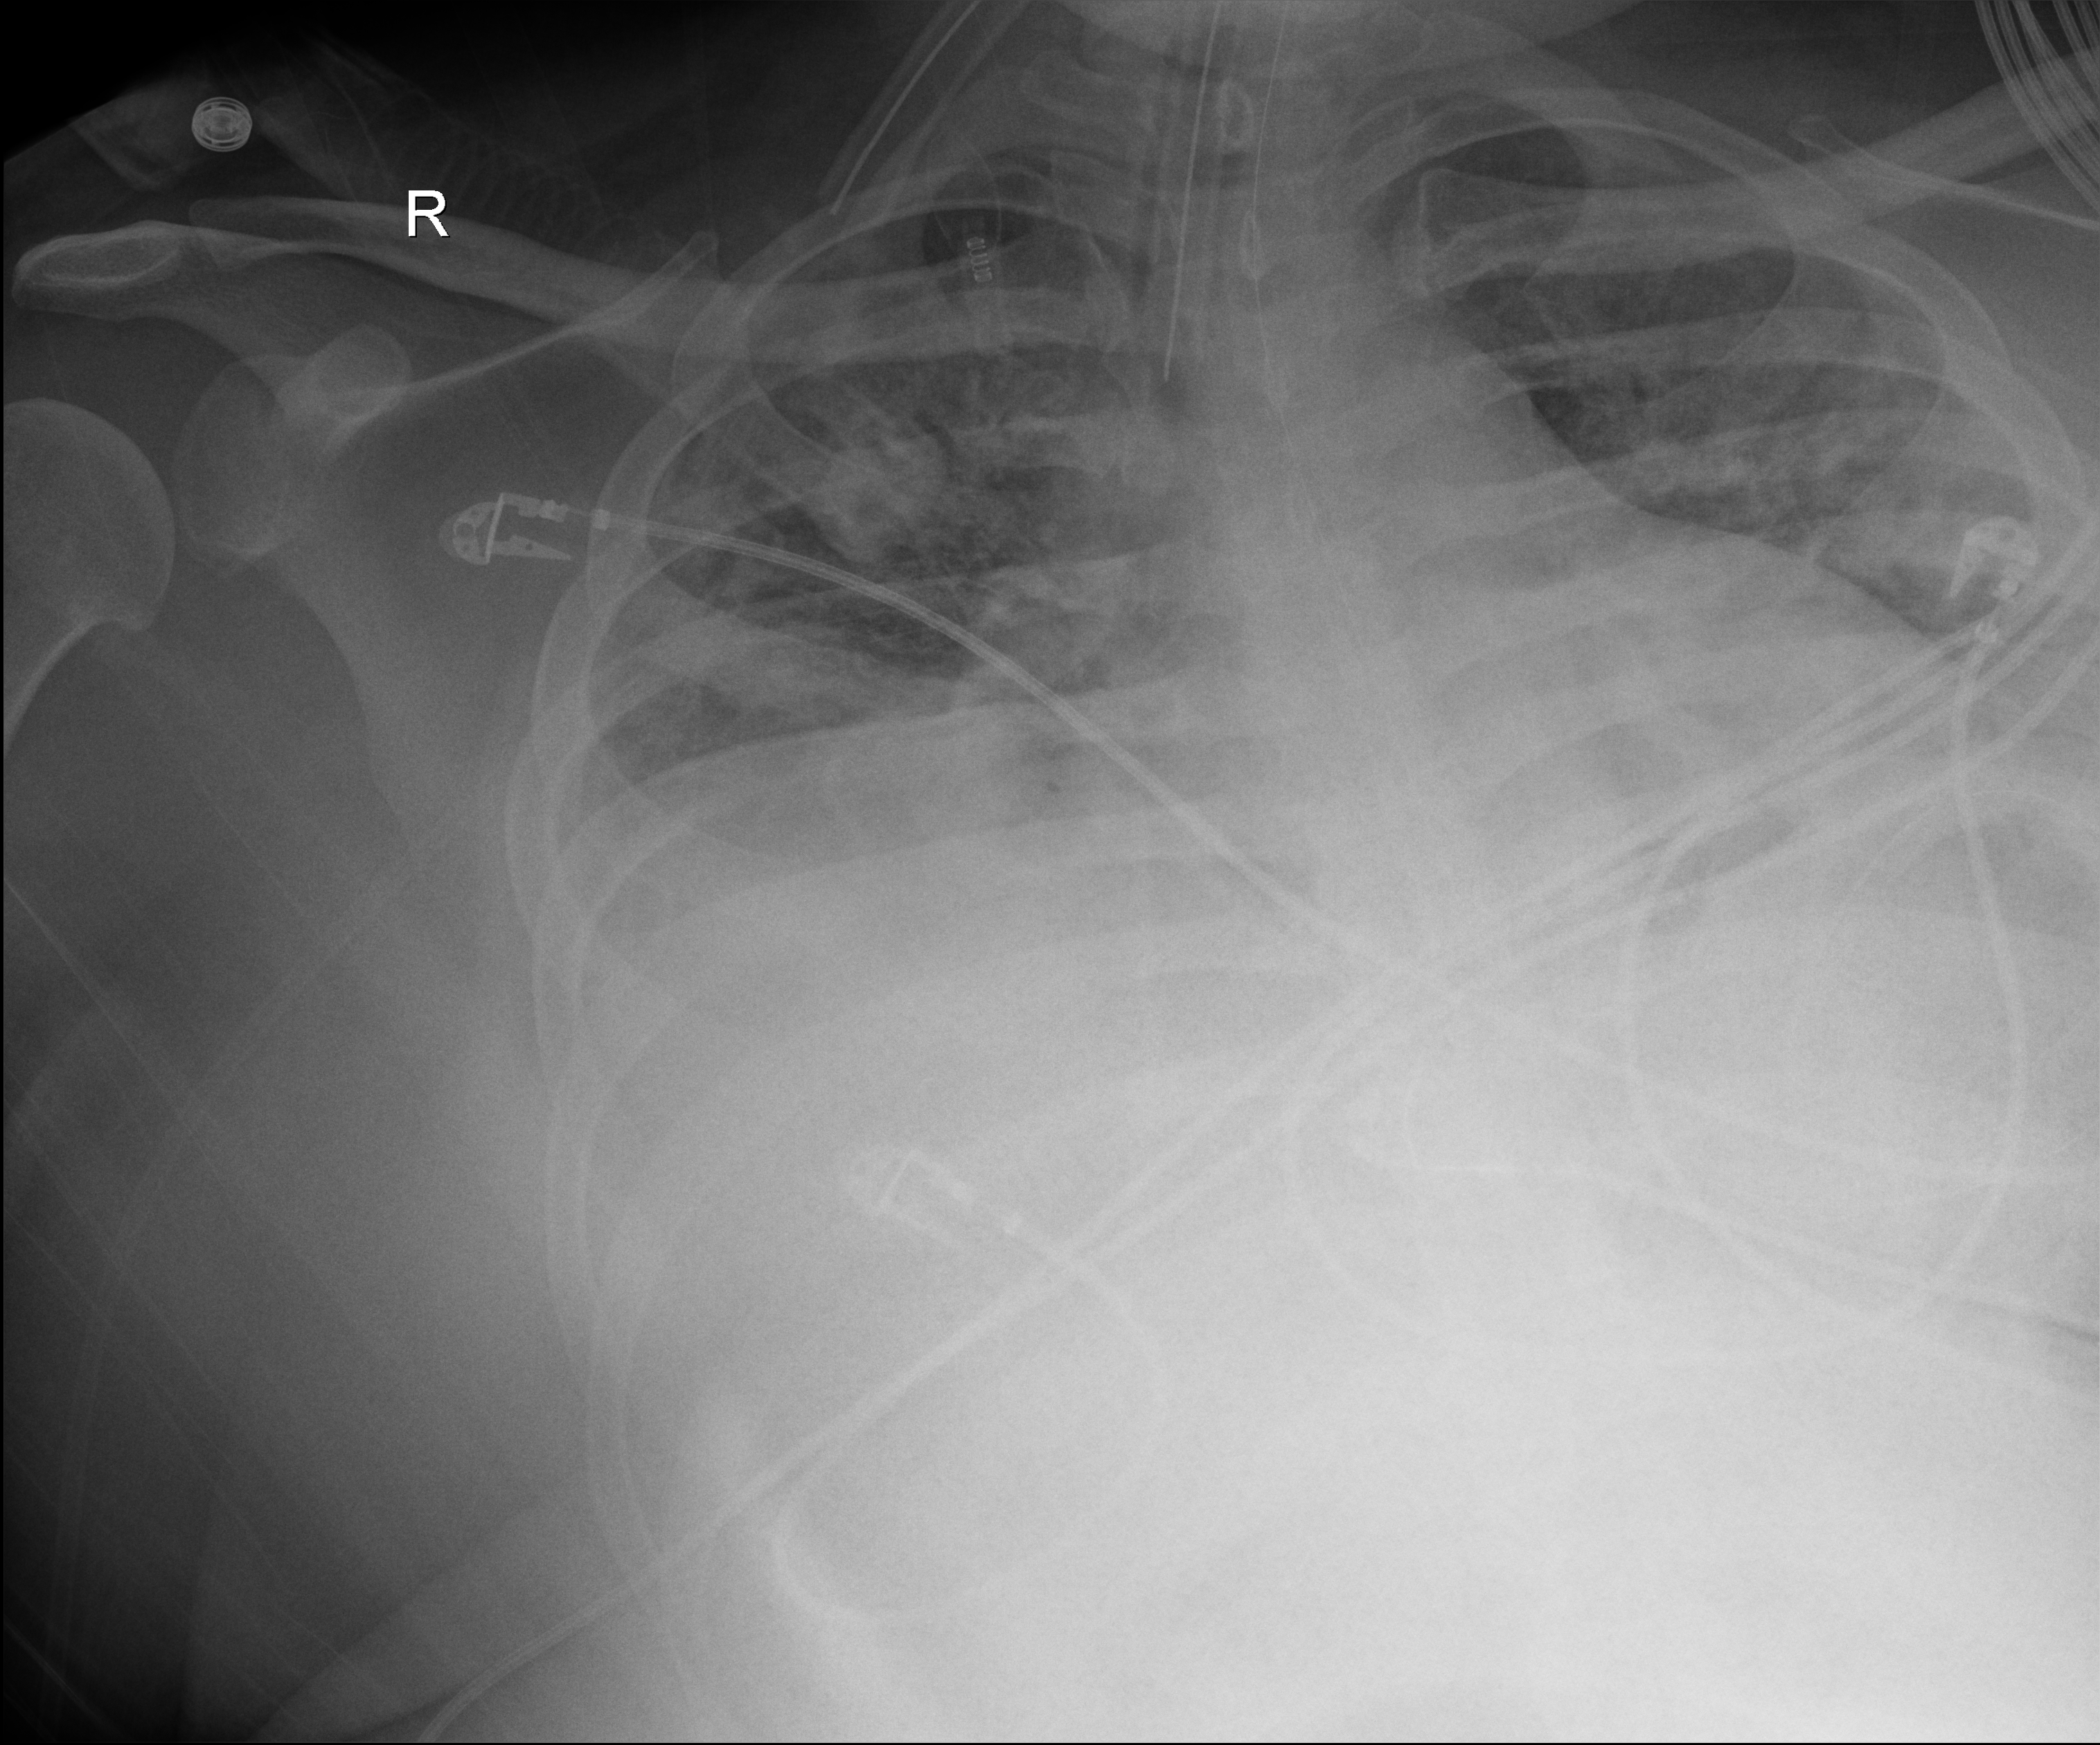
Chest radiograph (digital radiography). Patient hospitalised with COVID-19; male, aged 18–59 years.
Admission-level facts for this patient (not findings on this image; timing relative to this image not recorded): admitted to intensive care during this hospital stay: yes.